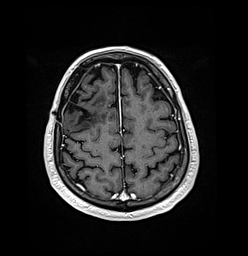
Brain MRI from a brain-tumour surgery series, one axial slice; position 42 of 176 along the scan axis; T1-weighted post-contrast; 1 mm slice thickness; 248 × 256 image matrix. Case-level facts recorded for this patient, not image findings: histopathology: Oligodendroglioma; WHO grade: 3; IDH mutation: yes; tumour location: Right Frontal.
Annotated regions visible in this slice (manually delineated by an expert):
- previous resection cavity: bounding box (x1, y1, x2, y2) in pixels: (65, 91, 90, 125)